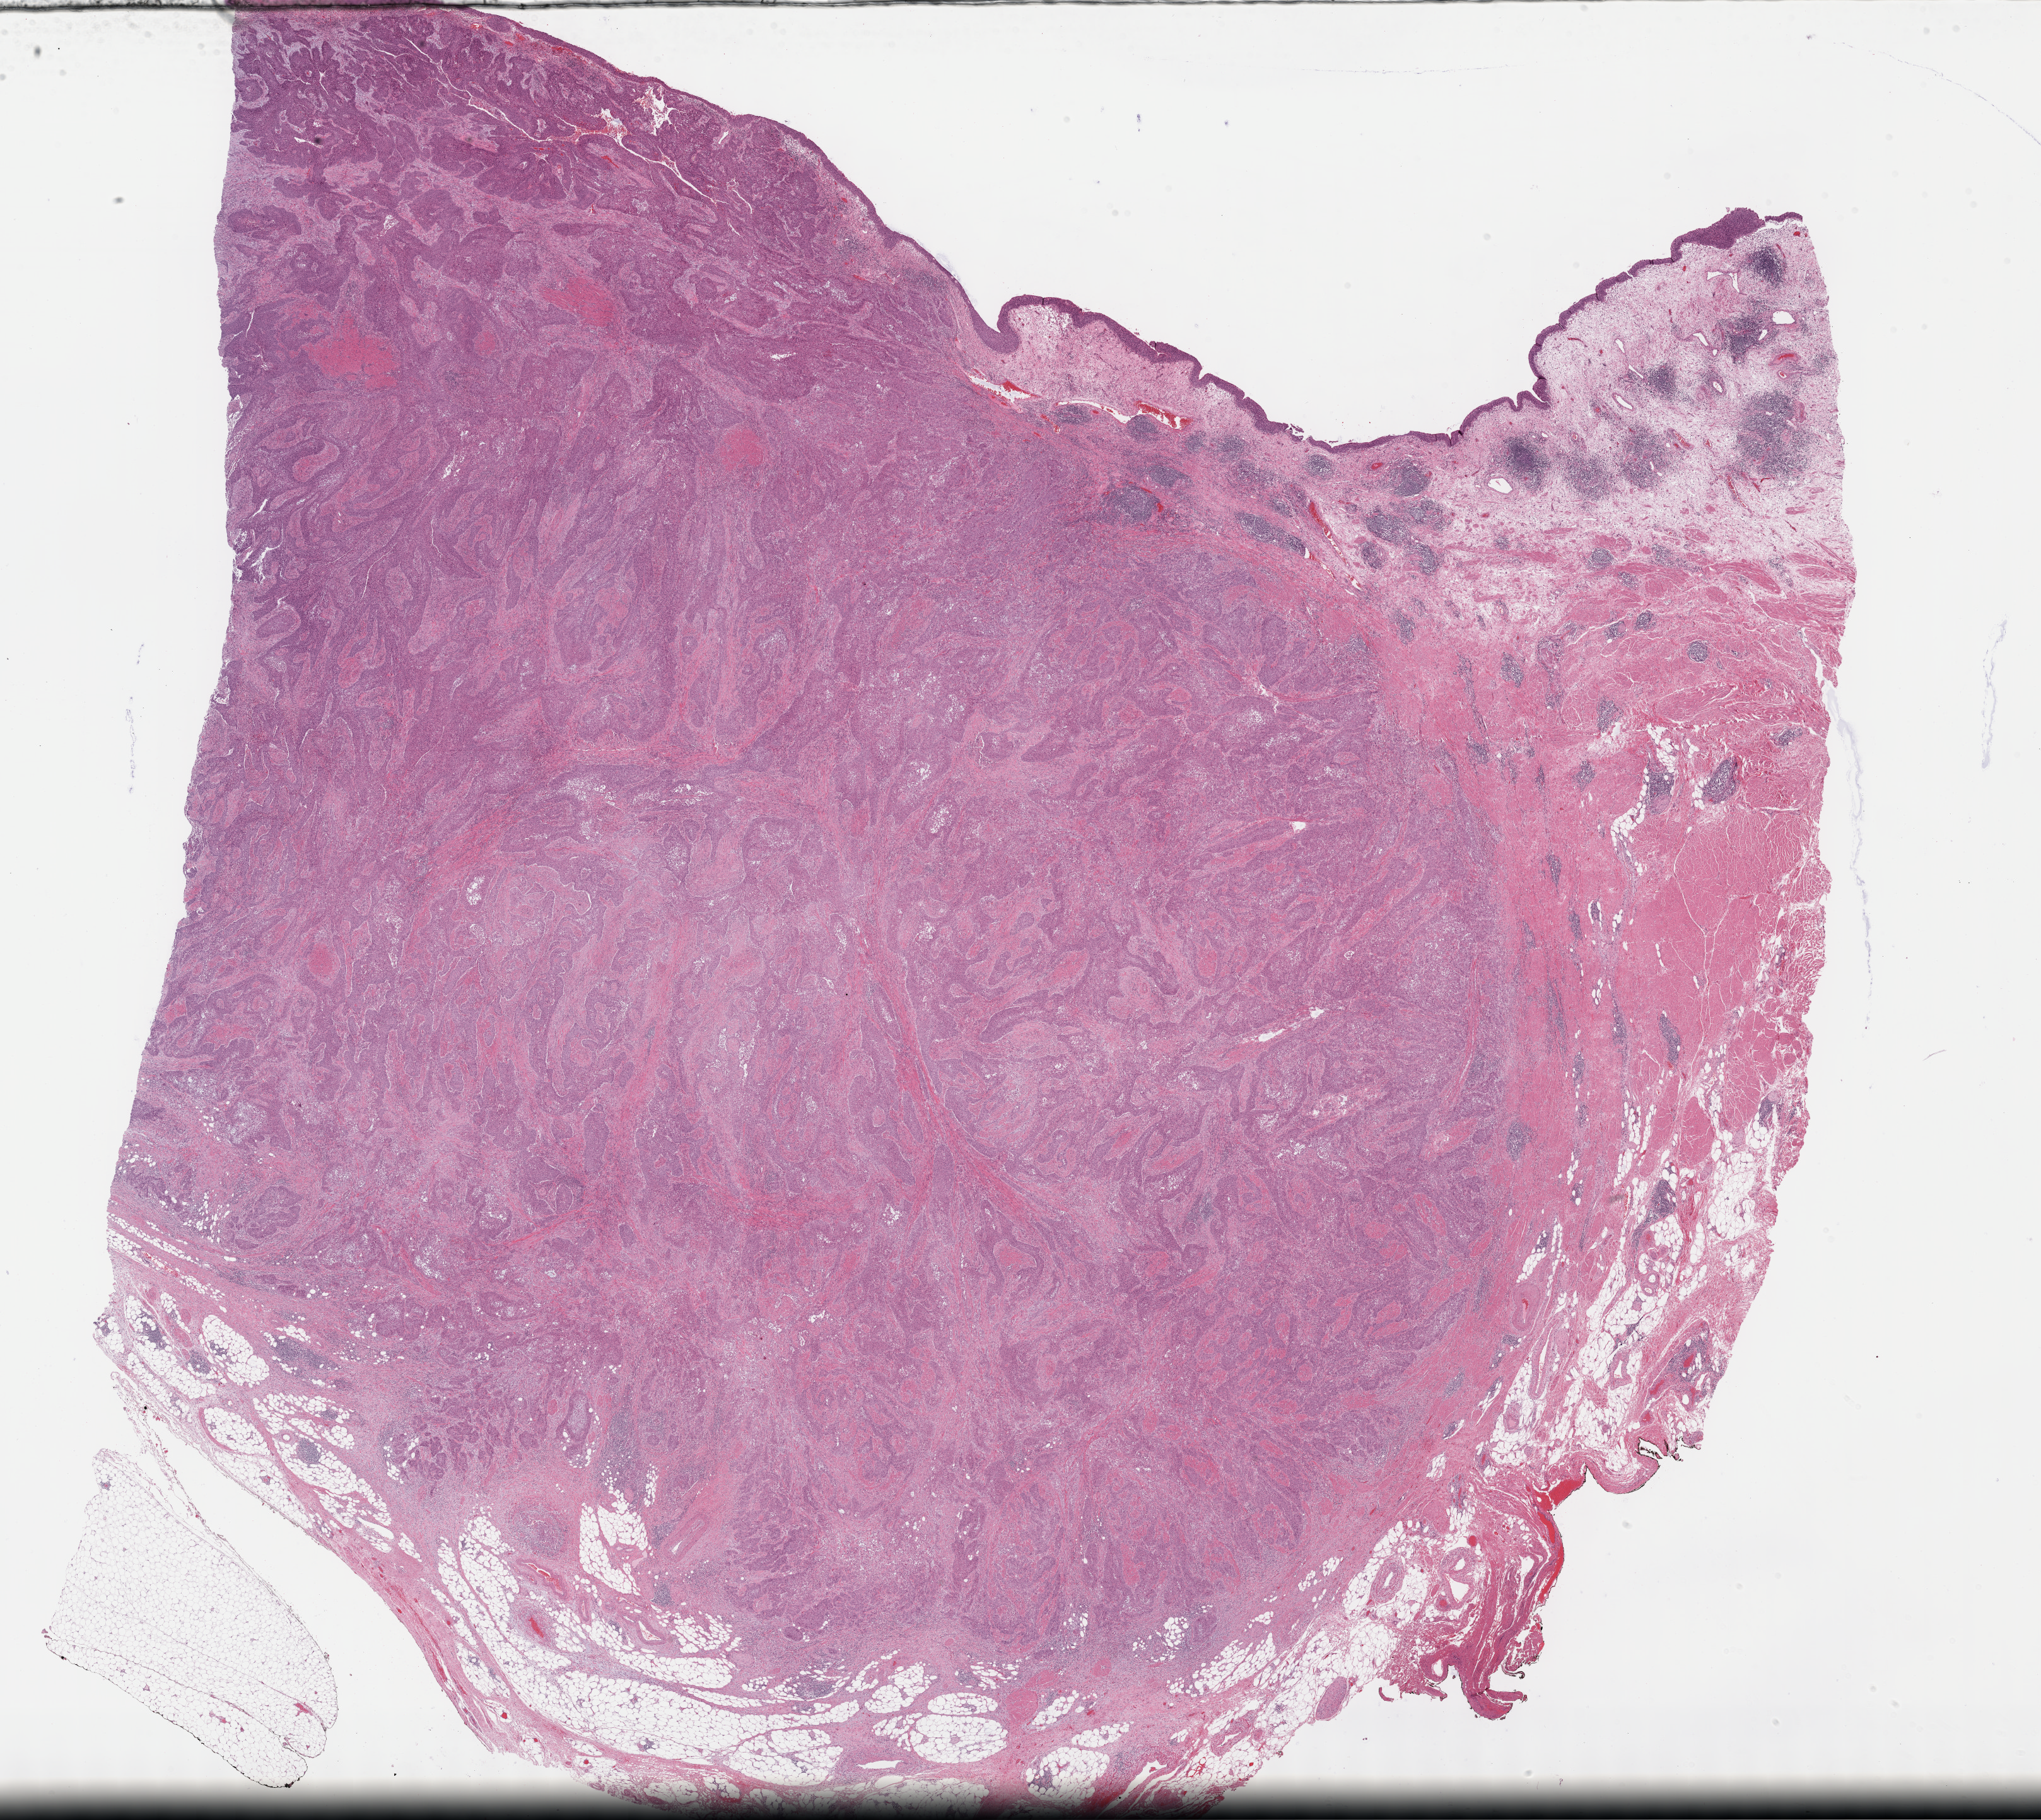
Digitized H&E-stained tissue section (whole slide) — low-resolution overview of the scanned area, about 26.2 x 23.3 mm, FFPE section, sample: primary tumour, bladder. Female, age 71 years at initial diagnosis. Histologic grade: high grade.
Diagnosis: Transitional cell carcinoma (posterior wall of bladder). TNM: T3b N0 MX. Lymph nodes positive (case pathology): 0 of 26 examined. AJCC pathologic stage: III (7th edition).